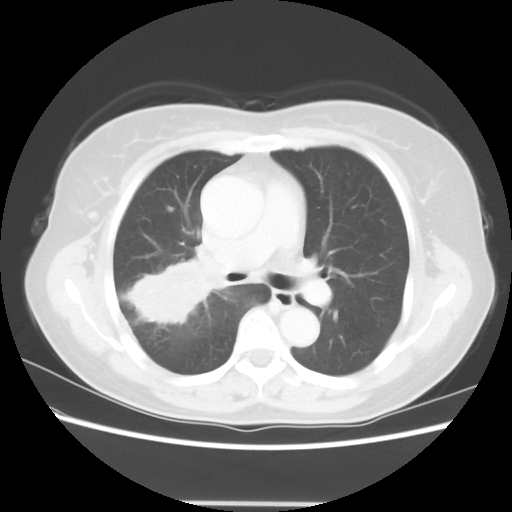
Chest CT, one axial slice. Slice 36 of 56 in the series (ordered by position). Reconstruction kernel STANDARD. 120 kVp. Lung window (W 1500 / L -600 HU). 5 mm slice thickness. 512 × 512 image matrix. Female patient, age 55 years. From the clinical record (not read from this slice): clinical TNM (as recorded): T2 N1 M0; histopathological grade: G2-3.
Annotated regions visible in this slice (bounding box drawn by a radiologist):
- lung tumour (recorded histology: adenocarcinoma): bounding box <122,260,222,330> (left, top, right, bottom; pixels)